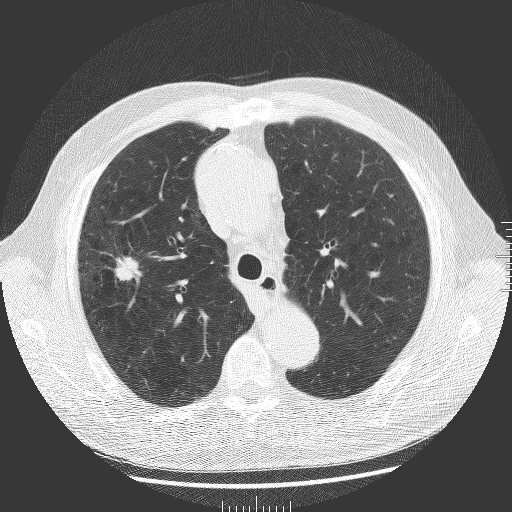
Low-dose screening chest CT, one axial slice; slice 132 of 181 in the series (ordered by position); reconstruction kernel BONE; 120 kVp; lung window (W 1500 / L -600 HU); 2 mm slice thickness; 512 × 512 image matrix, field of view 380 × 380 mm.
Outlined on this slice (expert manual segmentation):
- lesion 1 (tumor, upper lobe of right lung): box from (x=115, y=257) to (x=141, y=281) px